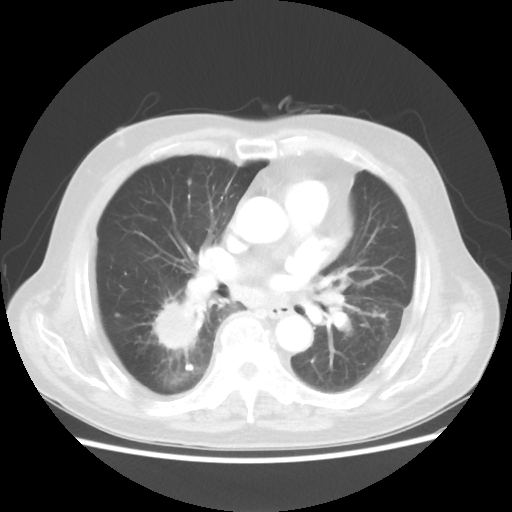
Chest CT, one axial slice; slice 20 of 44 in the series (ordered by position); reconstruction kernel STANDARD; 100 kVp; lung window (W 1500 / L -600 HU); 5 mm slice thickness; 512 × 512 image matrix, field of view 359 × 359 mm. Patient: male, 83 years. Case-level facts recorded for this patient, not image findings: clinical TNM (as recorded): T2 N3 M0.
Structures marked on this image (bounding box drawn by a radiologist):
- lung tumour (recorded histology: adenocarcinoma): box from (x=139, y=284) to (x=206, y=358) px